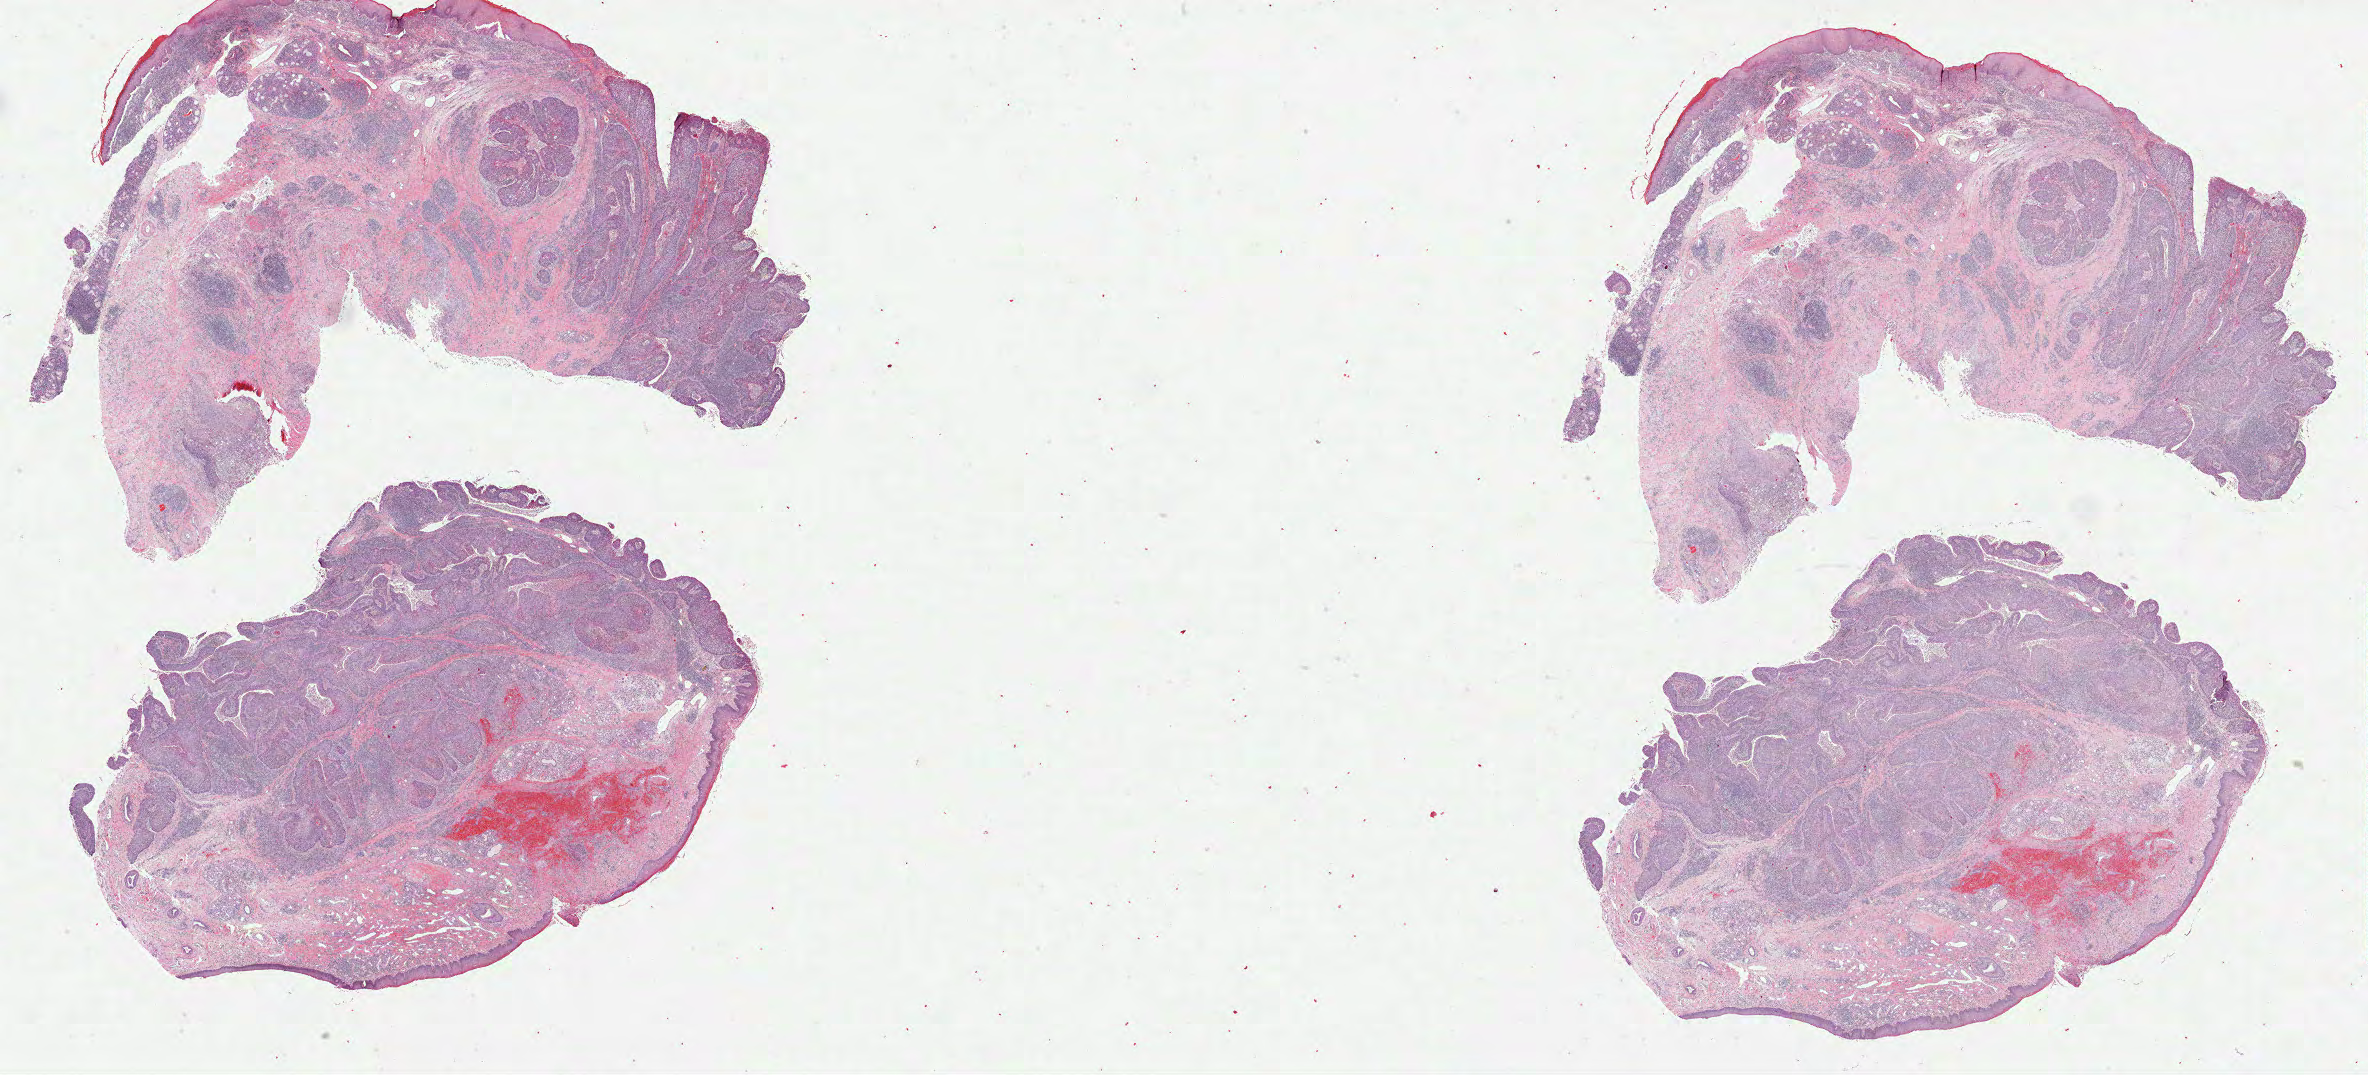
H&E-stained whole-slide image, a low-resolution overview of the entire scanned area, about 38.2 x 17.3 mm (from a 40x scan), formalin-fixed paraffin-embedded (FFPE) diagnostic section, sample: primary tumour, head and neck. Male, age 71 years at initial diagnosis. Histologic grade: G2 (moderately differentiated).
- AJCC pathologic stage: IVA (6th edition)
- lymph nodes positive (case pathology): 0 of 54 examined
- pathologic diagnosis: Squamous cell carcinoma, NOS (larynx, NOS)
- TNM: T4a N0 M0